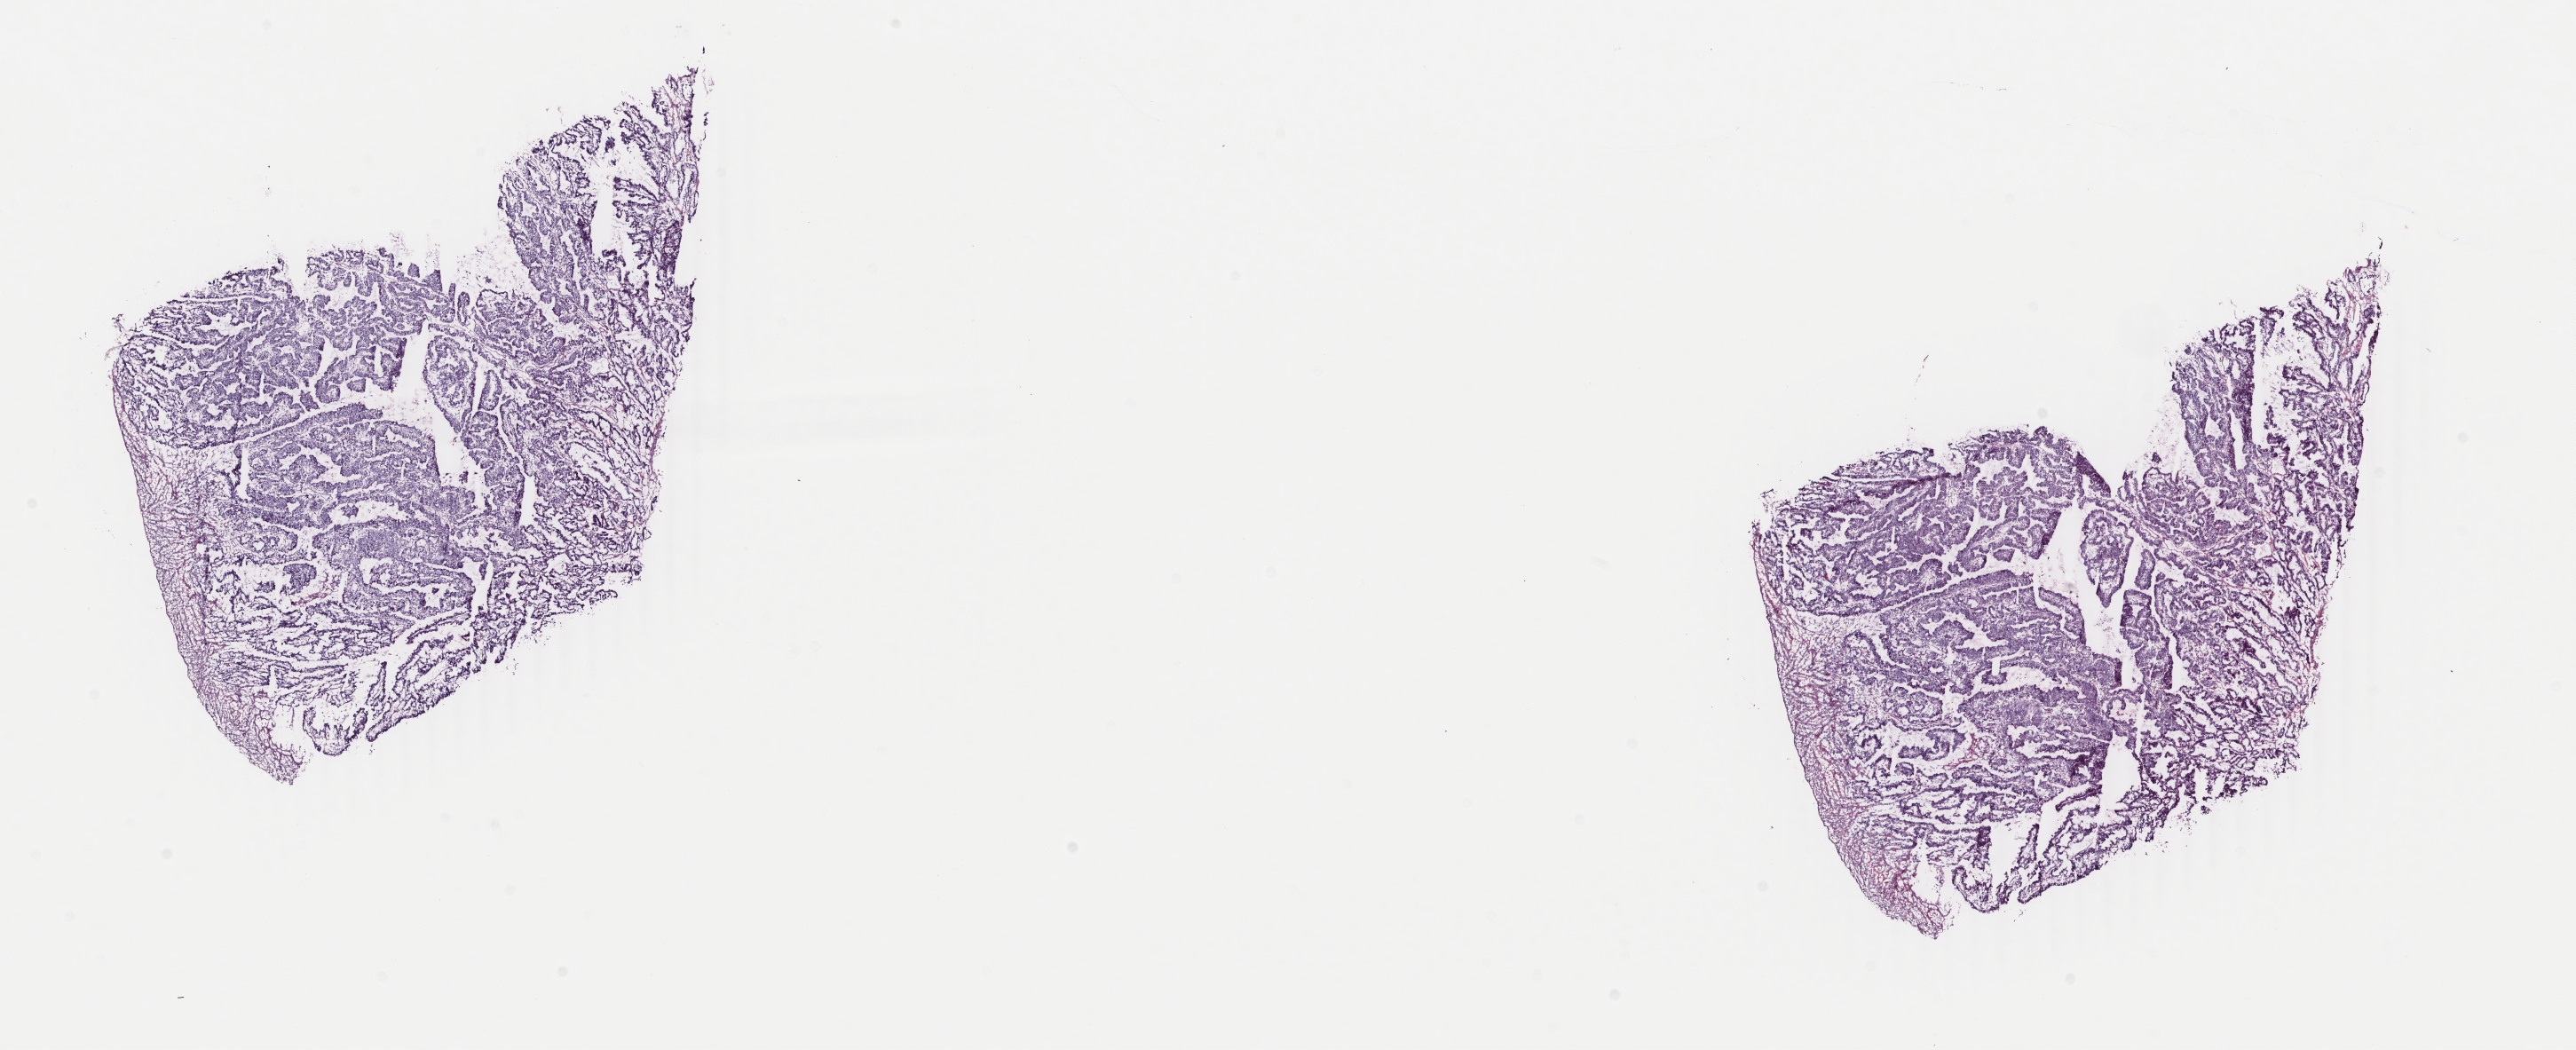
Digitized H&E tissue section (whole slide) — low-resolution overview of the scanned area, about 23.1 x 9.4 mm. Frozen section from the top of the tissue portion. Primary tumour sample from the esophagus. Male, age 56 years at initial diagnosis. Histologic grade: G1 (well differentiated). Slide review estimates, as recorded: tumour cells 80%, tumour nuclei 100%, normal cells 0%, stromal cells 20%, necrosis 0%. Inflammatory infiltration, as recorded: lymphocyte infiltration 2%, monocyte infiltration 0%, neutrophil infiltration 0%.
- lymph nodes positive (case pathology): 0 of 12 examined
- diagnosis: Adenocarcinoma, NOS (lower third of esophagus)
- AJCC pathologic stage: I (6th edition)